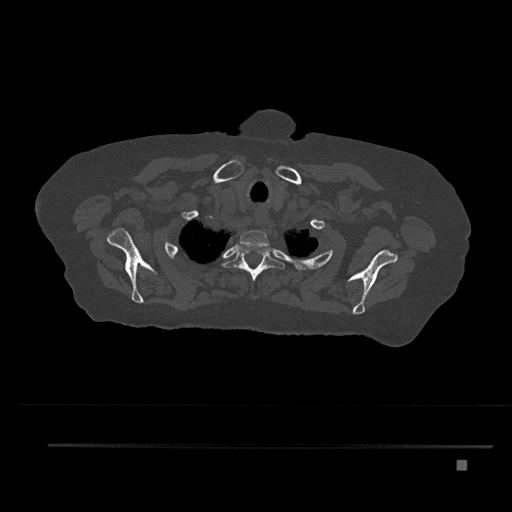
CT including the spine, one axial slice. Position 676 of 797 along the scan axis. Reconstruction kernel Br40s/3. 120 kVp. Bone window (W 1800 / L 400 HU). 0.5 mm slice thickness. 512 × 512 image matrix. Female patient, age 76 years. Case-level facts recorded for this patient, not image findings: primary cancer: lung.
Annotated regions visible in this slice (semi-automatically segmented with operator editing):
- T1 vertebra: bounding box <240,230,269,248> (left, top, right, bottom; pixels)
- T2 vertebra: <222,244,285,281>